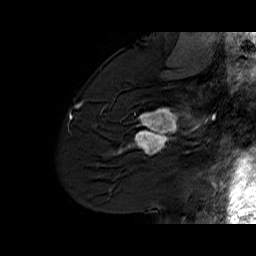
Breast MRI (dynamic contrast-enhanced), one sagittal slice; slice 43 of 60 in the series (ordered by position); dynamic contrast-enhanced series, time point 2 of 6 at this slice position (early post-contrast); 1.5 T; TE 6.1 ms, TR 32.9 ms; 4 mm slice thickness; 256 × 256 image matrix. Female patient. Case-level facts recorded for this patient, not image findings: setting: breast cancer imaged before/during neoadjuvant chemotherapy; receptor status: HER2-positive.
Annotated regions visible in this slice (semi-automatic segmentation, software-assisted and operator-edited):
- analysis volume of interest (the breast-tissue region the enhancement analysis was run in; not a lesion): bounding box (x1, y1, x2, y2) in pixels: (127, 95, 194, 165)
- tumour enhancement mask (voxels above the 100 % enhancement threshold inside the analysis volume of interest): (127, 108, 194, 154)